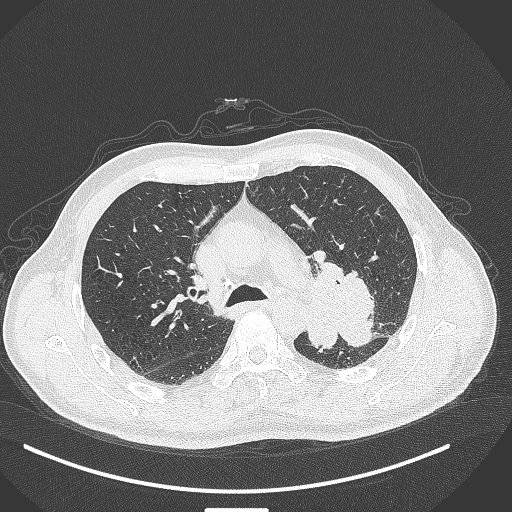
Chest CT, one axial slice; slice 279 of 429 in the series (ordered by position); lung window (W 1500 / L -600 HU); 1 mm slice thickness; 512 × 512 image matrix, field of view 400 × 400 mm. Patient: male, 55 years. From the clinical record (not read from this slice): clinical TNM (as recorded): T3 N0 M1c; histopathological grade: G3.
Annotated regions visible in this slice (bounding box drawn by a radiologist):
- lung tumour (recorded histology: adenocarcinoma): bounding box <311,261,382,355> (left, top, right, bottom; pixels)